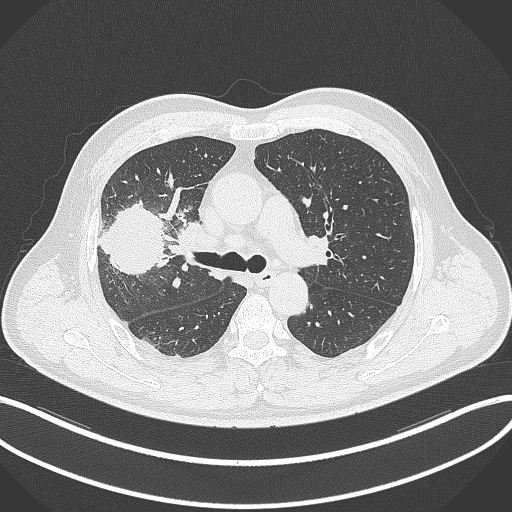
Chest CT, one axial slice. Slice 212 of 348 in the series (ordered by position). Reconstruction kernel B70f. 120 kVp. Lung window (W 1500 / L -600 HU). 1 mm slice thickness. 512 × 512 image matrix. Patient: male, 55 years. Case-level facts recorded for this patient, not image findings: clinical TNM (as recorded): T3 N2 M1.
Outlined on this slice (bounding box drawn by a radiologist):
- lung tumour (recorded histology: adenocarcinoma): bounding box [x1, y1, x2, y2] px = [94, 194, 170, 279]